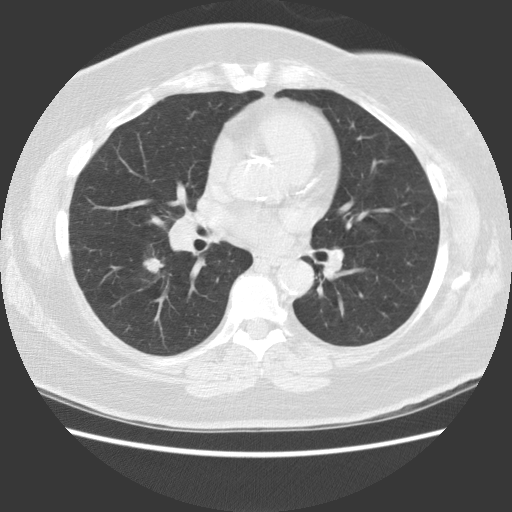
Low-dose screening chest CT, one axial slice. Slice 58 of 117 in the series (ordered by position). Reconstruction kernel STANDARD. 140 kVp. Lung window (W 1500 / L -600 HU). 2.5 mm slice thickness. 512 × 512 image matrix.
Structures marked on this image (outlined manually by an expert reader):
- lesion 1 (tumor, lower lobe of right lung): bounding box [x1, y1, x2, y2] px = [143, 257, 164, 273]